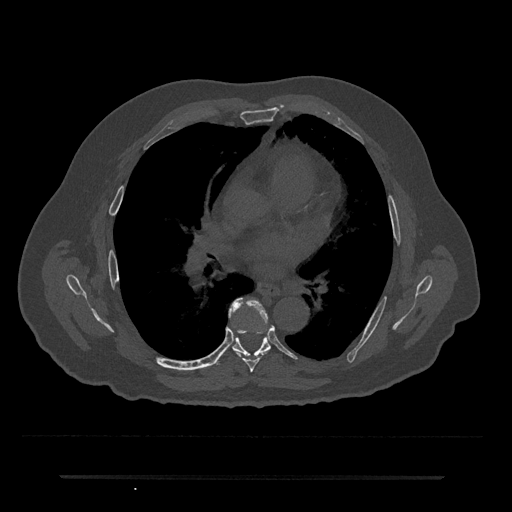
CT including the spine, one axial slice; position 412 of 797 along the scan axis; reconstruction kernel Br40s/3; 120 kVp; bone window (W 1800 / L 400 HU); 0.5 mm slice thickness; 512 × 512 image matrix, field of view 437 × 437 mm. Patient: male, 69 years. Case-level facts recorded for this patient, not image findings: primary cancer: prostate.
Outlined on this slice (semi-automatically segmented with operator editing):
- T6 vertebra: bounding box <230,298,267,372> (left, top, right, bottom; pixels)
- T7 vertebra: <215,331,271,365>